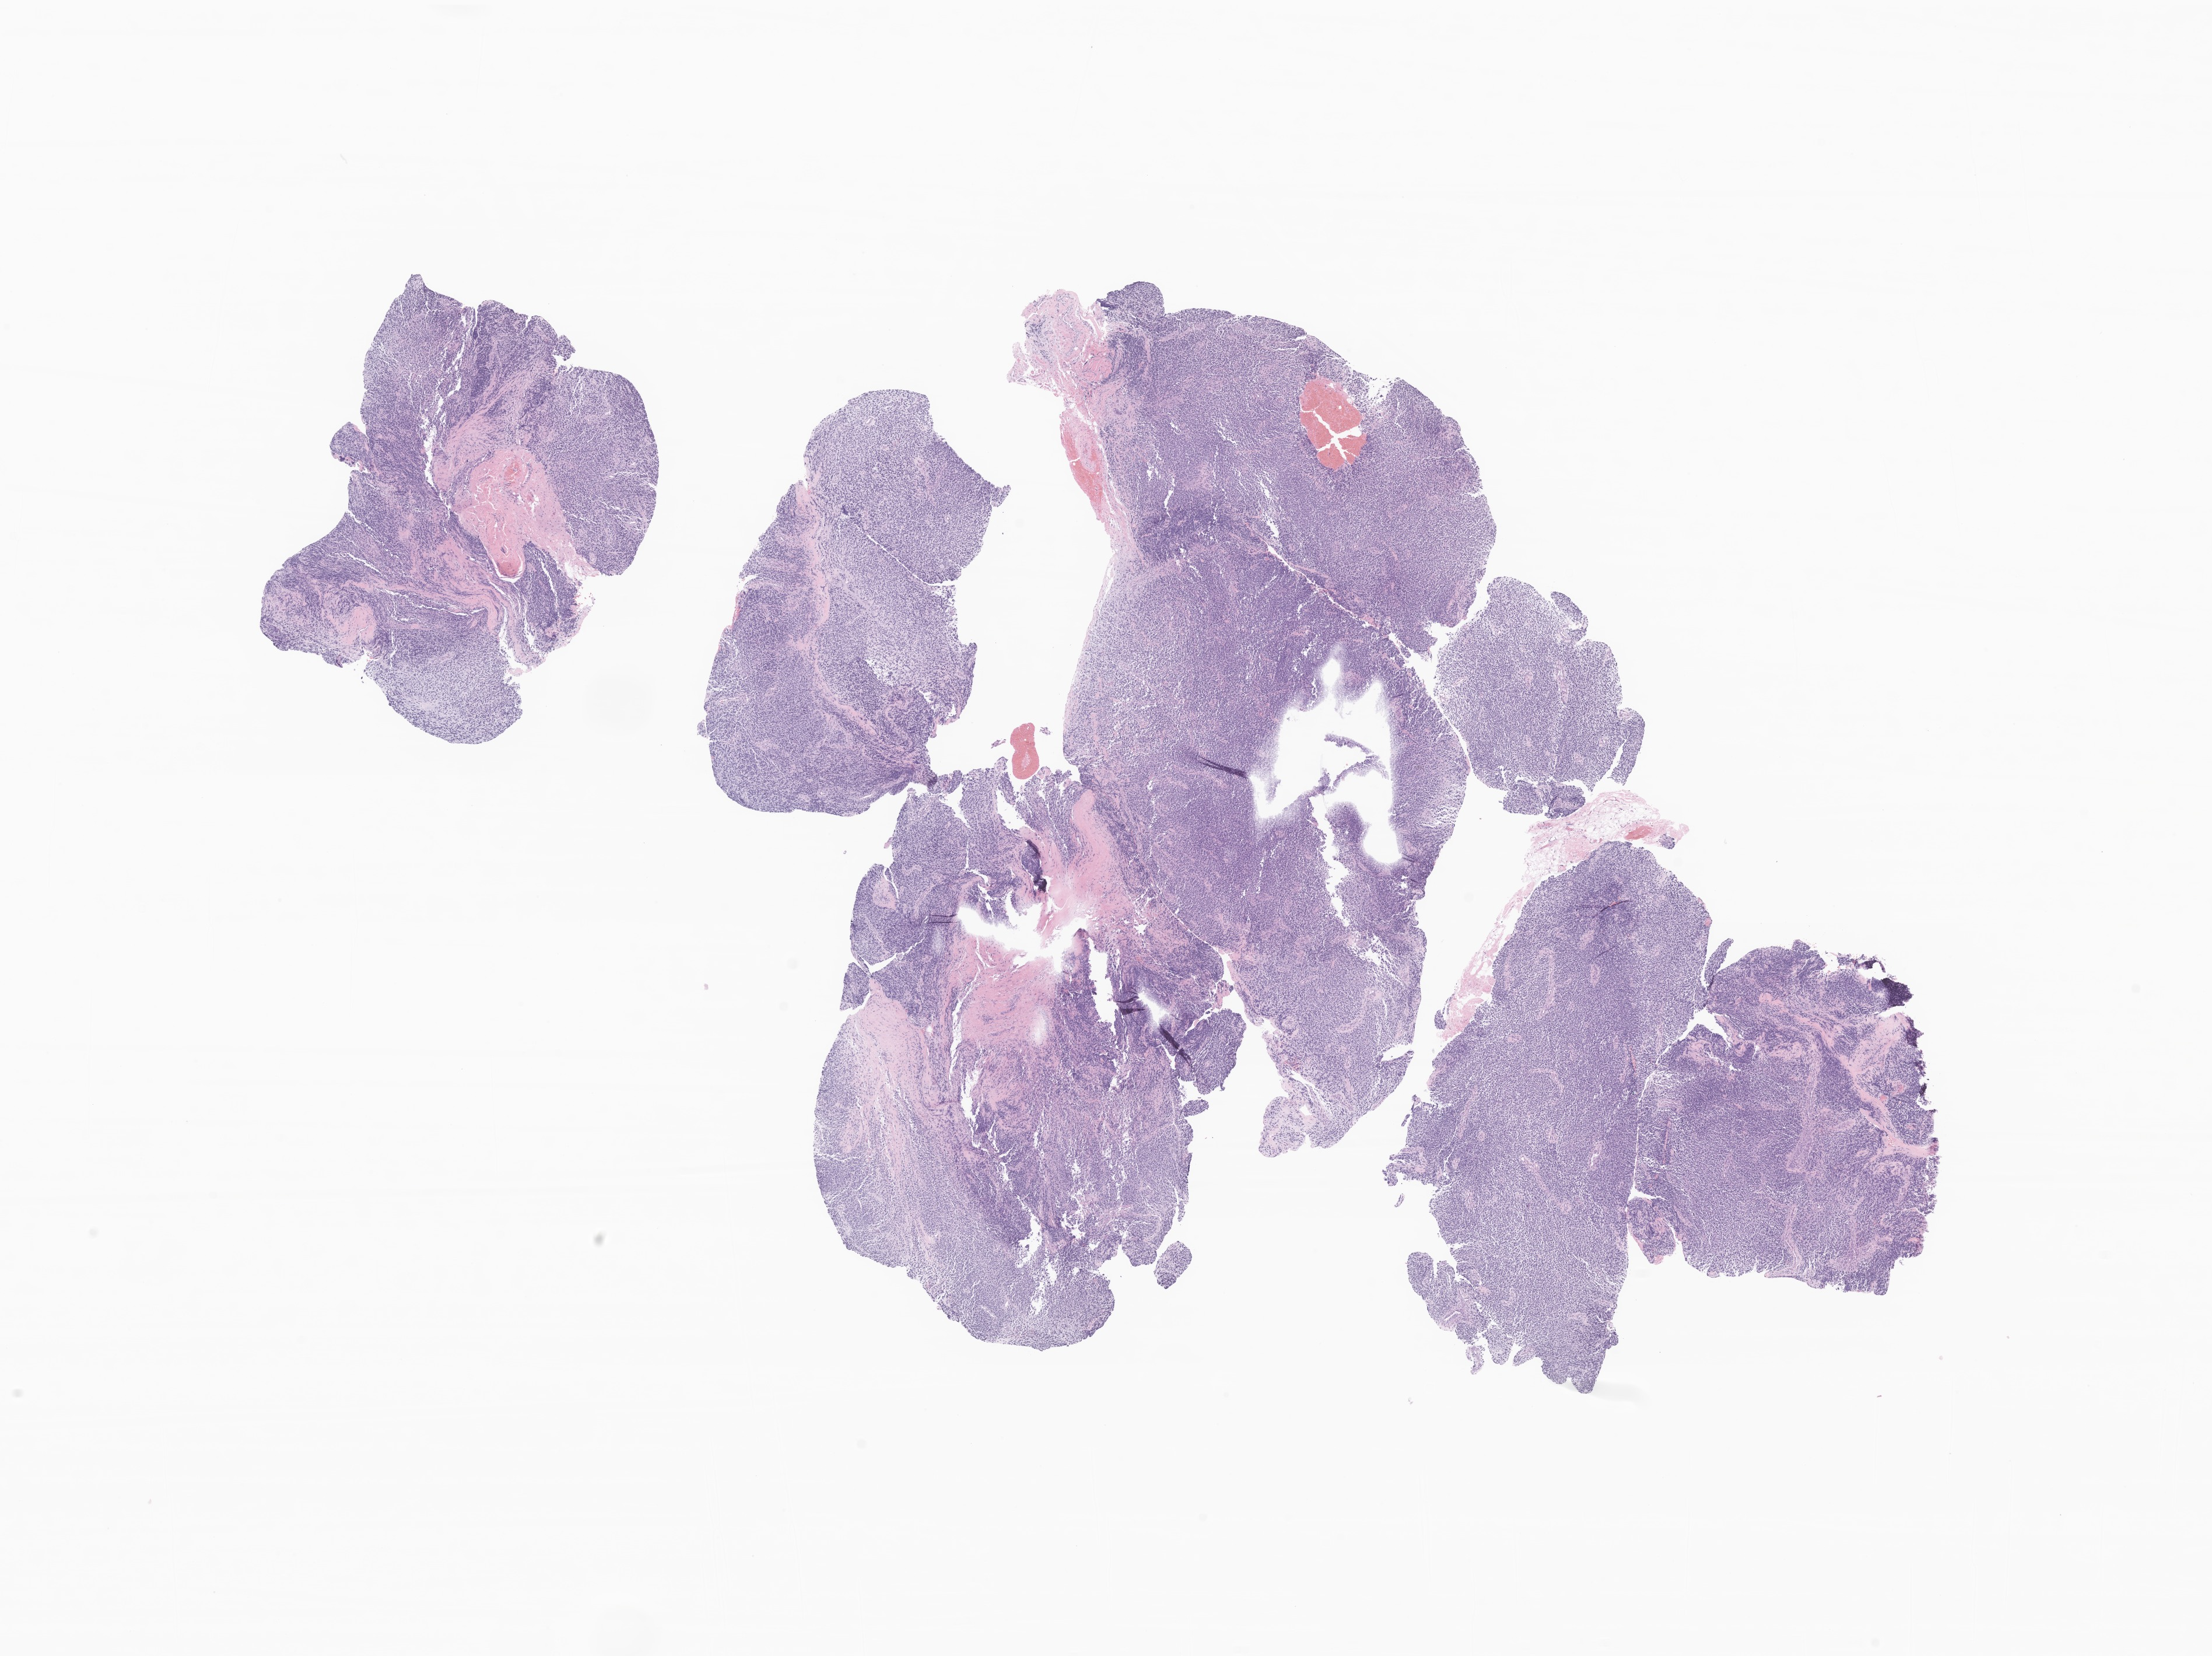
Digitized haematoxylin and eosin-stained section of tumor tissue from the eye, whole scanned area (about 16.0 x 12.0 mm) shown as a low-resolution overview; FFPE section. Female patient, age 142 months (11 years 10 months).
Recorded diagnosis: Rhabdomyosarcoma, NOS.